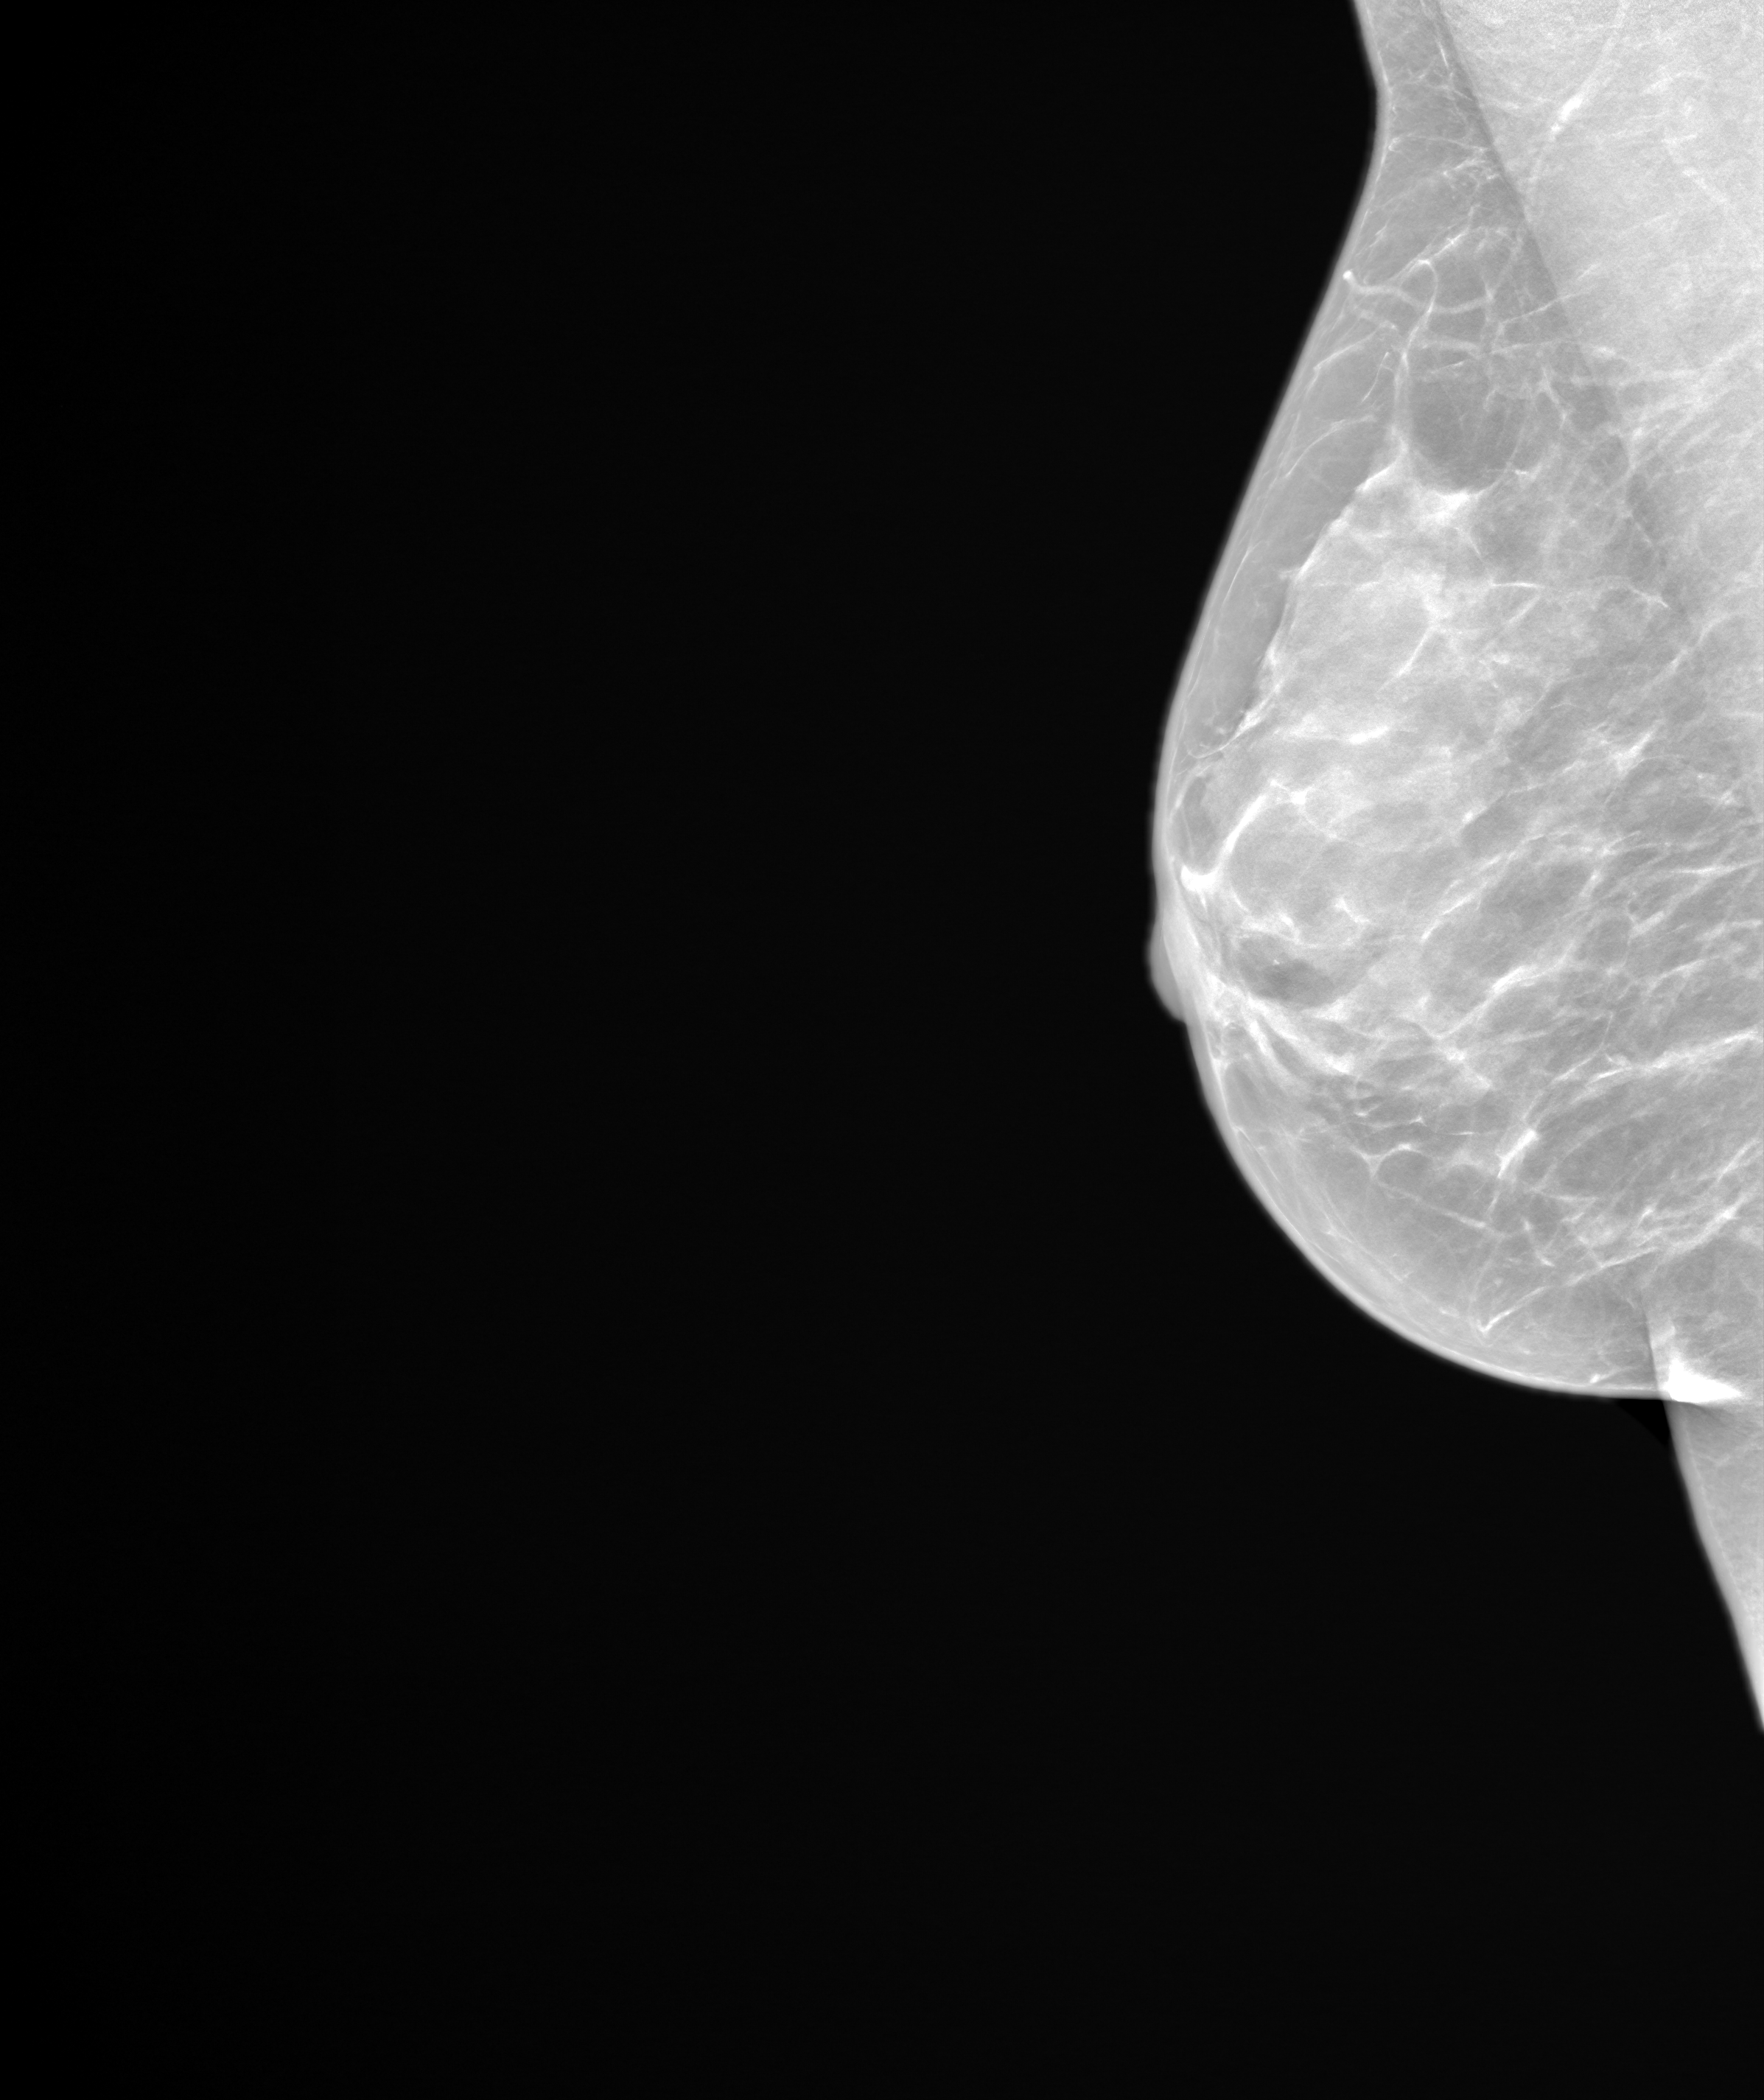
Annual screening mammography examination. Female patient, age 47 years.
Image type: synthesized 2-D view from tomosynthesis. Breast: right. Projection: medio-lateral oblique projection.